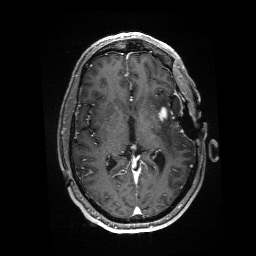
Brain MRI from a brain-tumour surgery series, one axial slice. Slice 86 of 176 in the series (ordered by position). T1-weighted post-contrast. 1 mm slice thickness. 256 × 256 image matrix, field of view 256 × 256 mm. From the clinical record (not read from this slice): histopathology: Glioblastoma; WHO grade: 4; IDH mutation: no; tumour location: Left Anterior/Superior Temporal.
Annotated regions visible in this slice (outlined manually by an expert reader):
- residual tumour: bounding box [x1, y1, x2, y2] px = [158, 106, 168, 121]